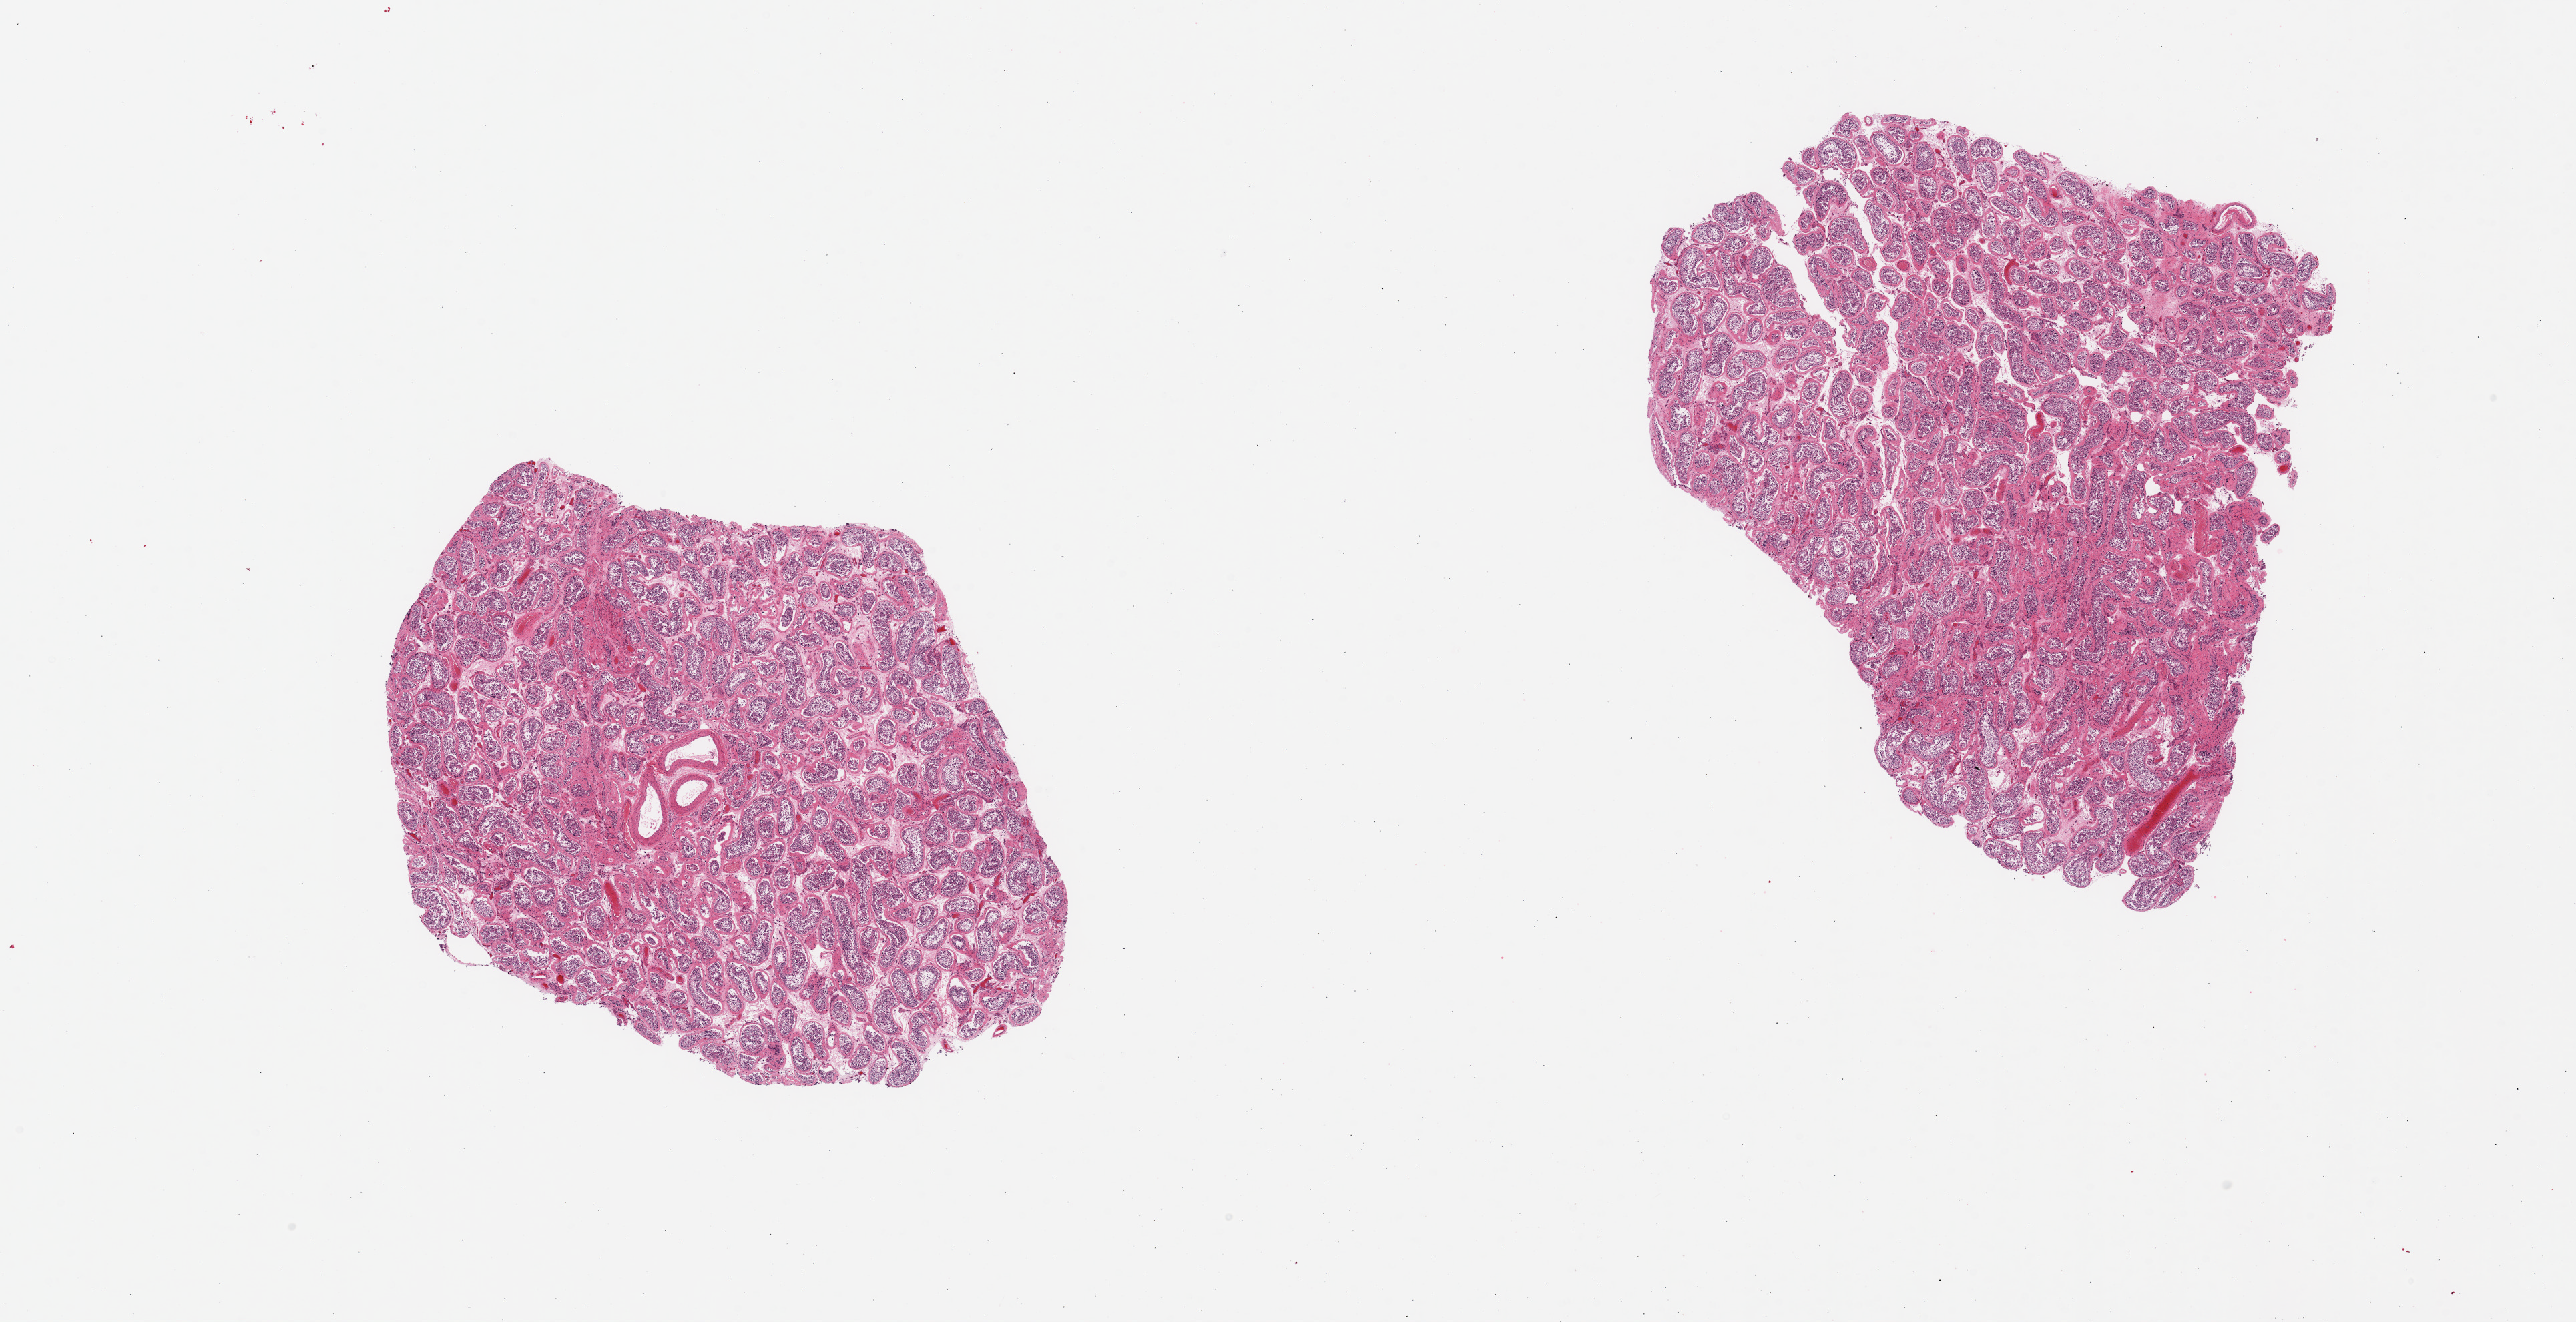
Digitized hematoxylin and eosin (H&E)-stained section — a low-resolution overview of the entire scanned area, about 30.5 x 15.7 mm (from a 20x scan), PAXgene-fixed, paraffin-embedded tissue, sampled site (target tissue): testis, donor tissue sample. Donor sex: male.
- pathologist's review note for this sample: 2 pieces, moderate tubular autolysis; spermatogenesis is present, appears reduced